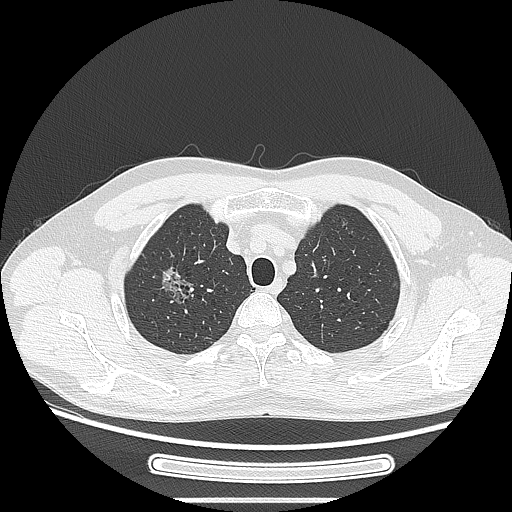
Chest CT, one axial slice; slice 220 of 269 in the series (ordered by position); reconstruction kernel LUNG; lung window (W 1500 / L -600 HU); 1.25 mm slice thickness; 512 × 512 image matrix, field of view 382 × 382 mm. Patient: male, 53 years. Case-level facts recorded for this patient, not image findings: clinical TNM (as recorded): T1c N0 M0.
Annotated regions visible in this slice (bounding box drawn by a radiologist):
- lung tumour (recorded histology: adenocarcinoma): bounding box [x1, y1, x2, y2] px = [148, 256, 200, 312]